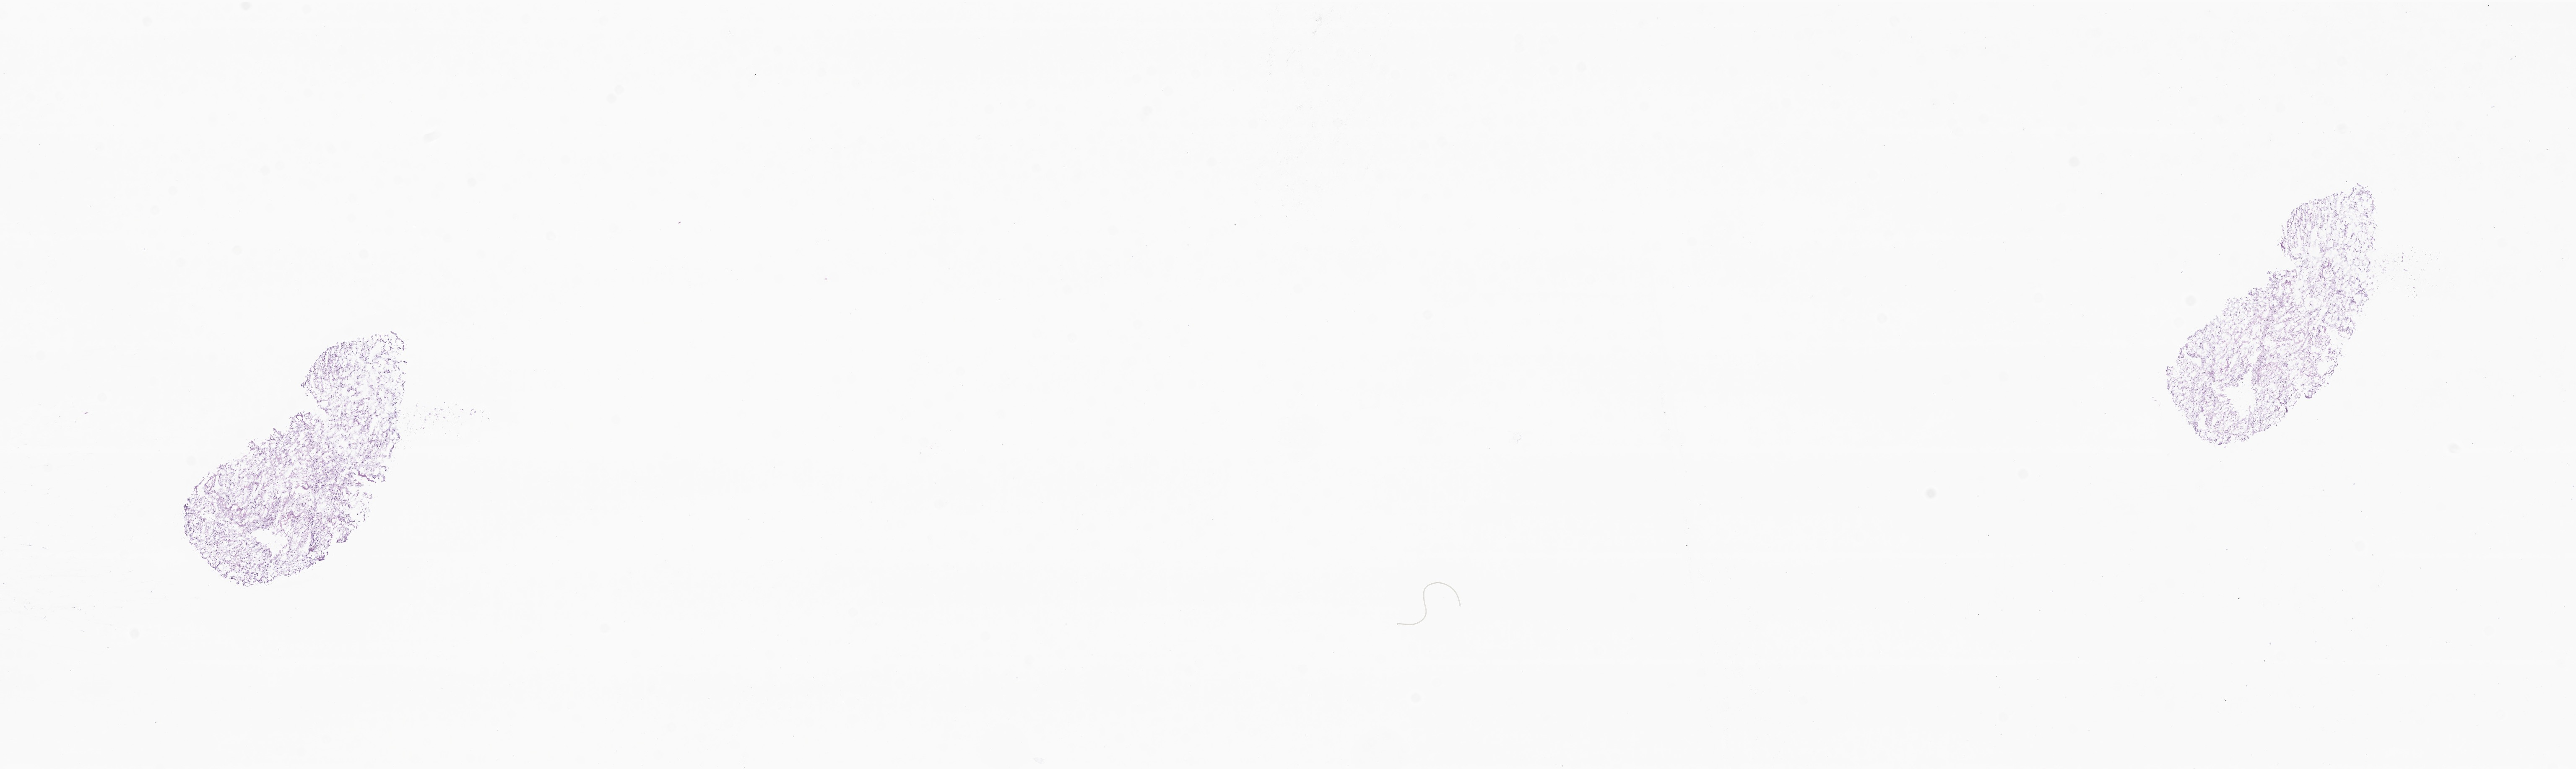
H&E whole-slide image of tumor tissue from the brain, whole scanned area (about 25.9 x 7.7 mm) shown as a low-resolution overview, frozen section (OCT-embedded). Patient: male, age 40 months (3 years 4 months).
Diagnosis: Pilocytic astrocytoma.